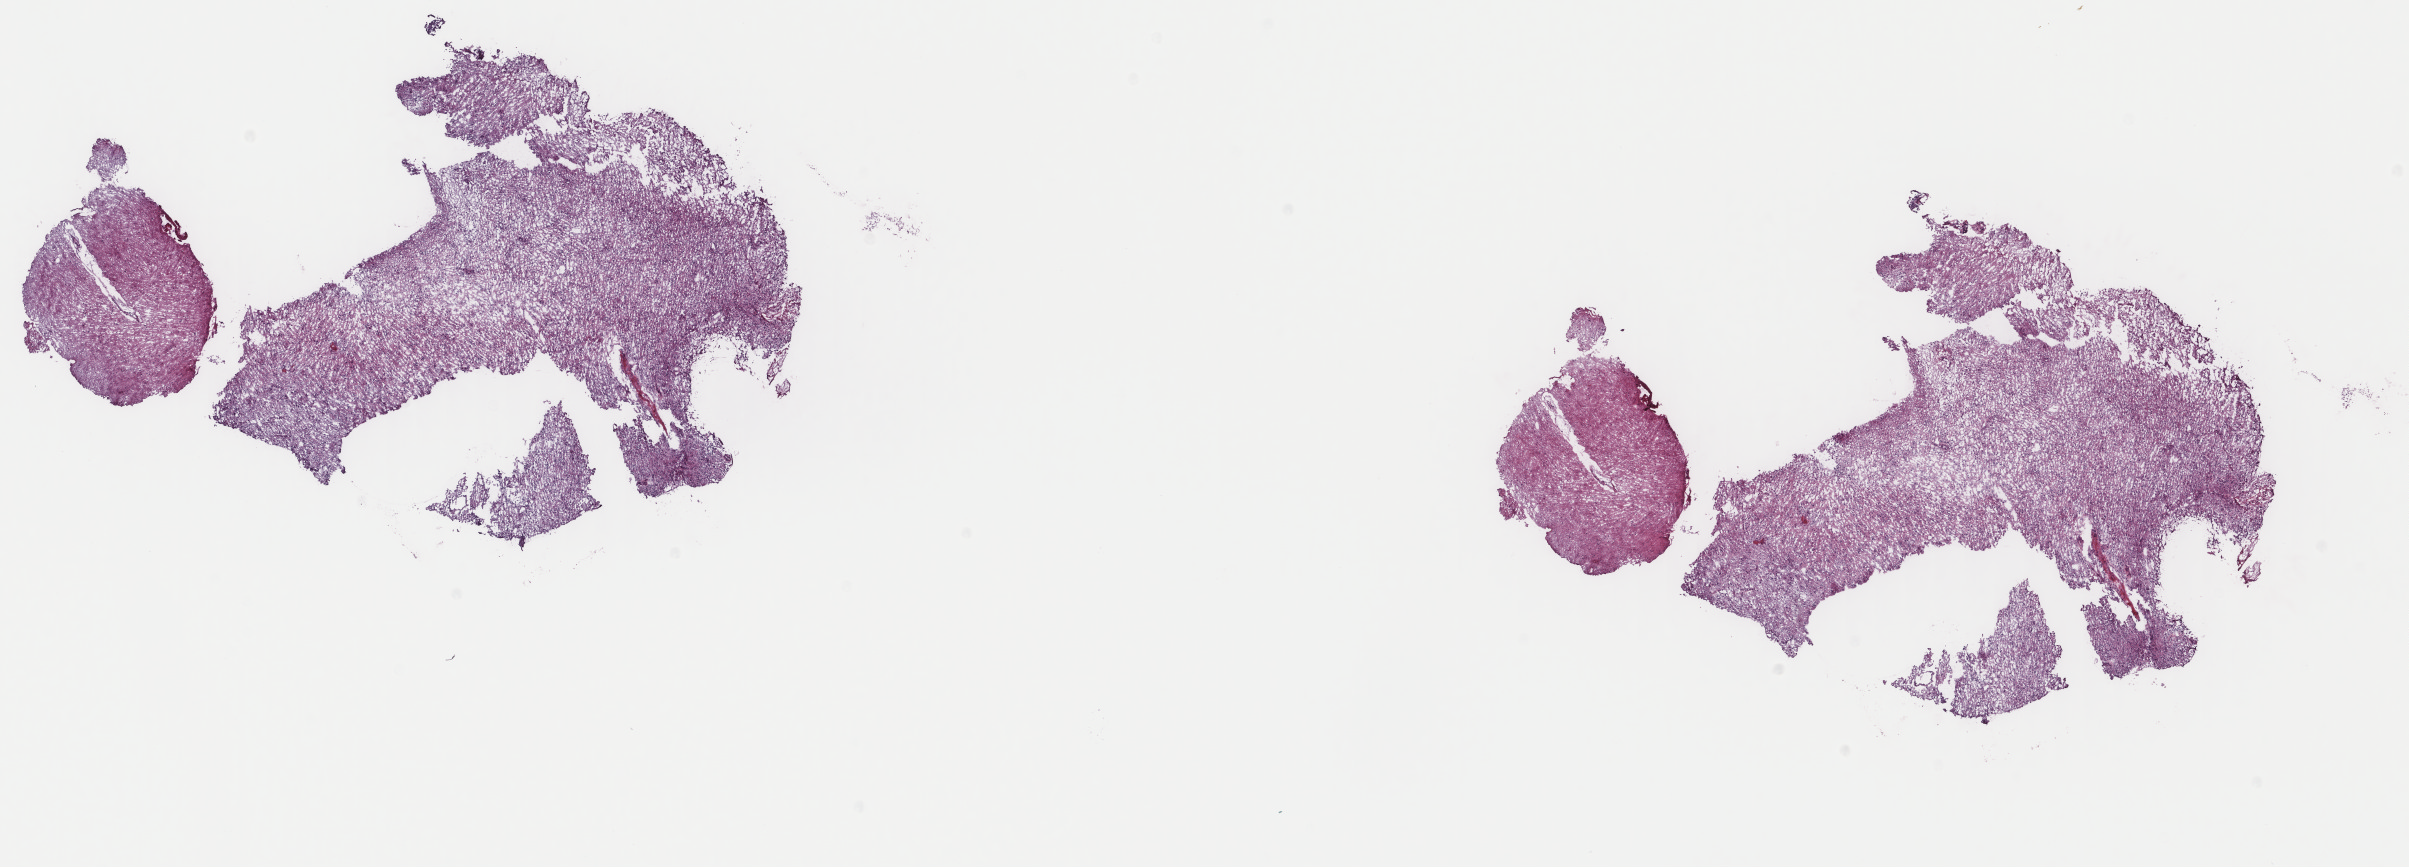
H&E whole-slide image — whole scanned area (about 19.1 x 6.9 mm, slide scanned at 40x) shown as a low-resolution overview, frozen section from the top of the tissue portion, primary tumour sample from the brain. Male, age 66 years at initial diagnosis. Histologic grade: G3 (poorly differentiated). Pathologist review of this section (percent, as recorded): tumour cells 70%, tumour nuclei 80%, normal cells 5%, stromal cells 25%, necrosis 0%. Inflammatory infiltration, as recorded: lymphocyte infiltration 0%, monocyte infiltration 0%, neutrophil infiltration 0%.
Diagnosis: Oligodendroglioma, anaplastic (cerebrum).